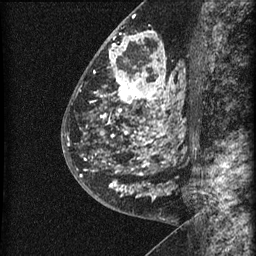
Breast MRI (dynamic contrast-enhanced), one sagittal slice. Slice 29 of 60 in the series (ordered by position). Dynamic contrast-enhanced series, image 2 of 3 at this slice position (ordered by acquisition). 1.5 T. TE 4.2 ms, TR 22.7 ms. 1.5 mm slice thickness. 256 × 256 image matrix, field of view 180 × 180 mm. Female patient, age 48 years. Case-level facts recorded for this patient, not image findings: setting: breast cancer imaged before/during neoadjuvant chemotherapy; receptor status: triple-negative.
Annotated regions visible in this slice (semi-automatic segmentation, software-assisted and operator-edited):
- analysis volume of interest (the breast-tissue region the enhancement analysis was run in; not a lesion): bounding box [x1, y1, x2, y2] px = [81, 23, 186, 202]
- tumour enhancement mask (voxels above the 90 % enhancement threshold inside the analysis volume of interest): [81, 32, 176, 197]